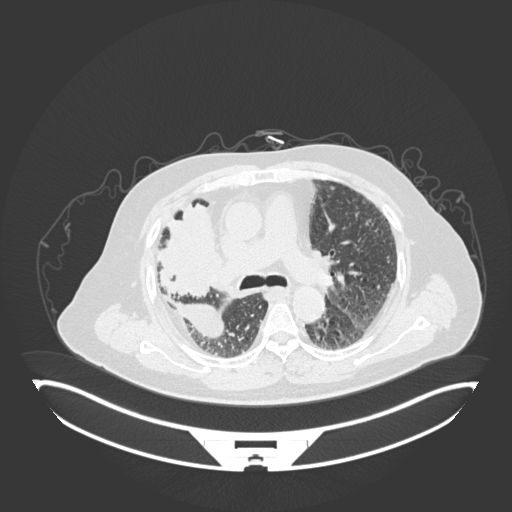
Chest CT, one axial slice; slice 107 of 201 in the series (ordered by position); reconstruction kernel B30f; lung window (W 1500 / L -600 HU); 1 mm slice thickness; 512 × 512 image matrix. Male patient, age 69 years. Case-level facts recorded for this patient, not image findings: clinical TNM (as recorded): T4 N3 M1.
Structures marked on this image (bounding box drawn by a radiologist):
- lung tumour (recorded histology: adenocarcinoma): box from (x=155, y=200) to (x=225, y=296) px